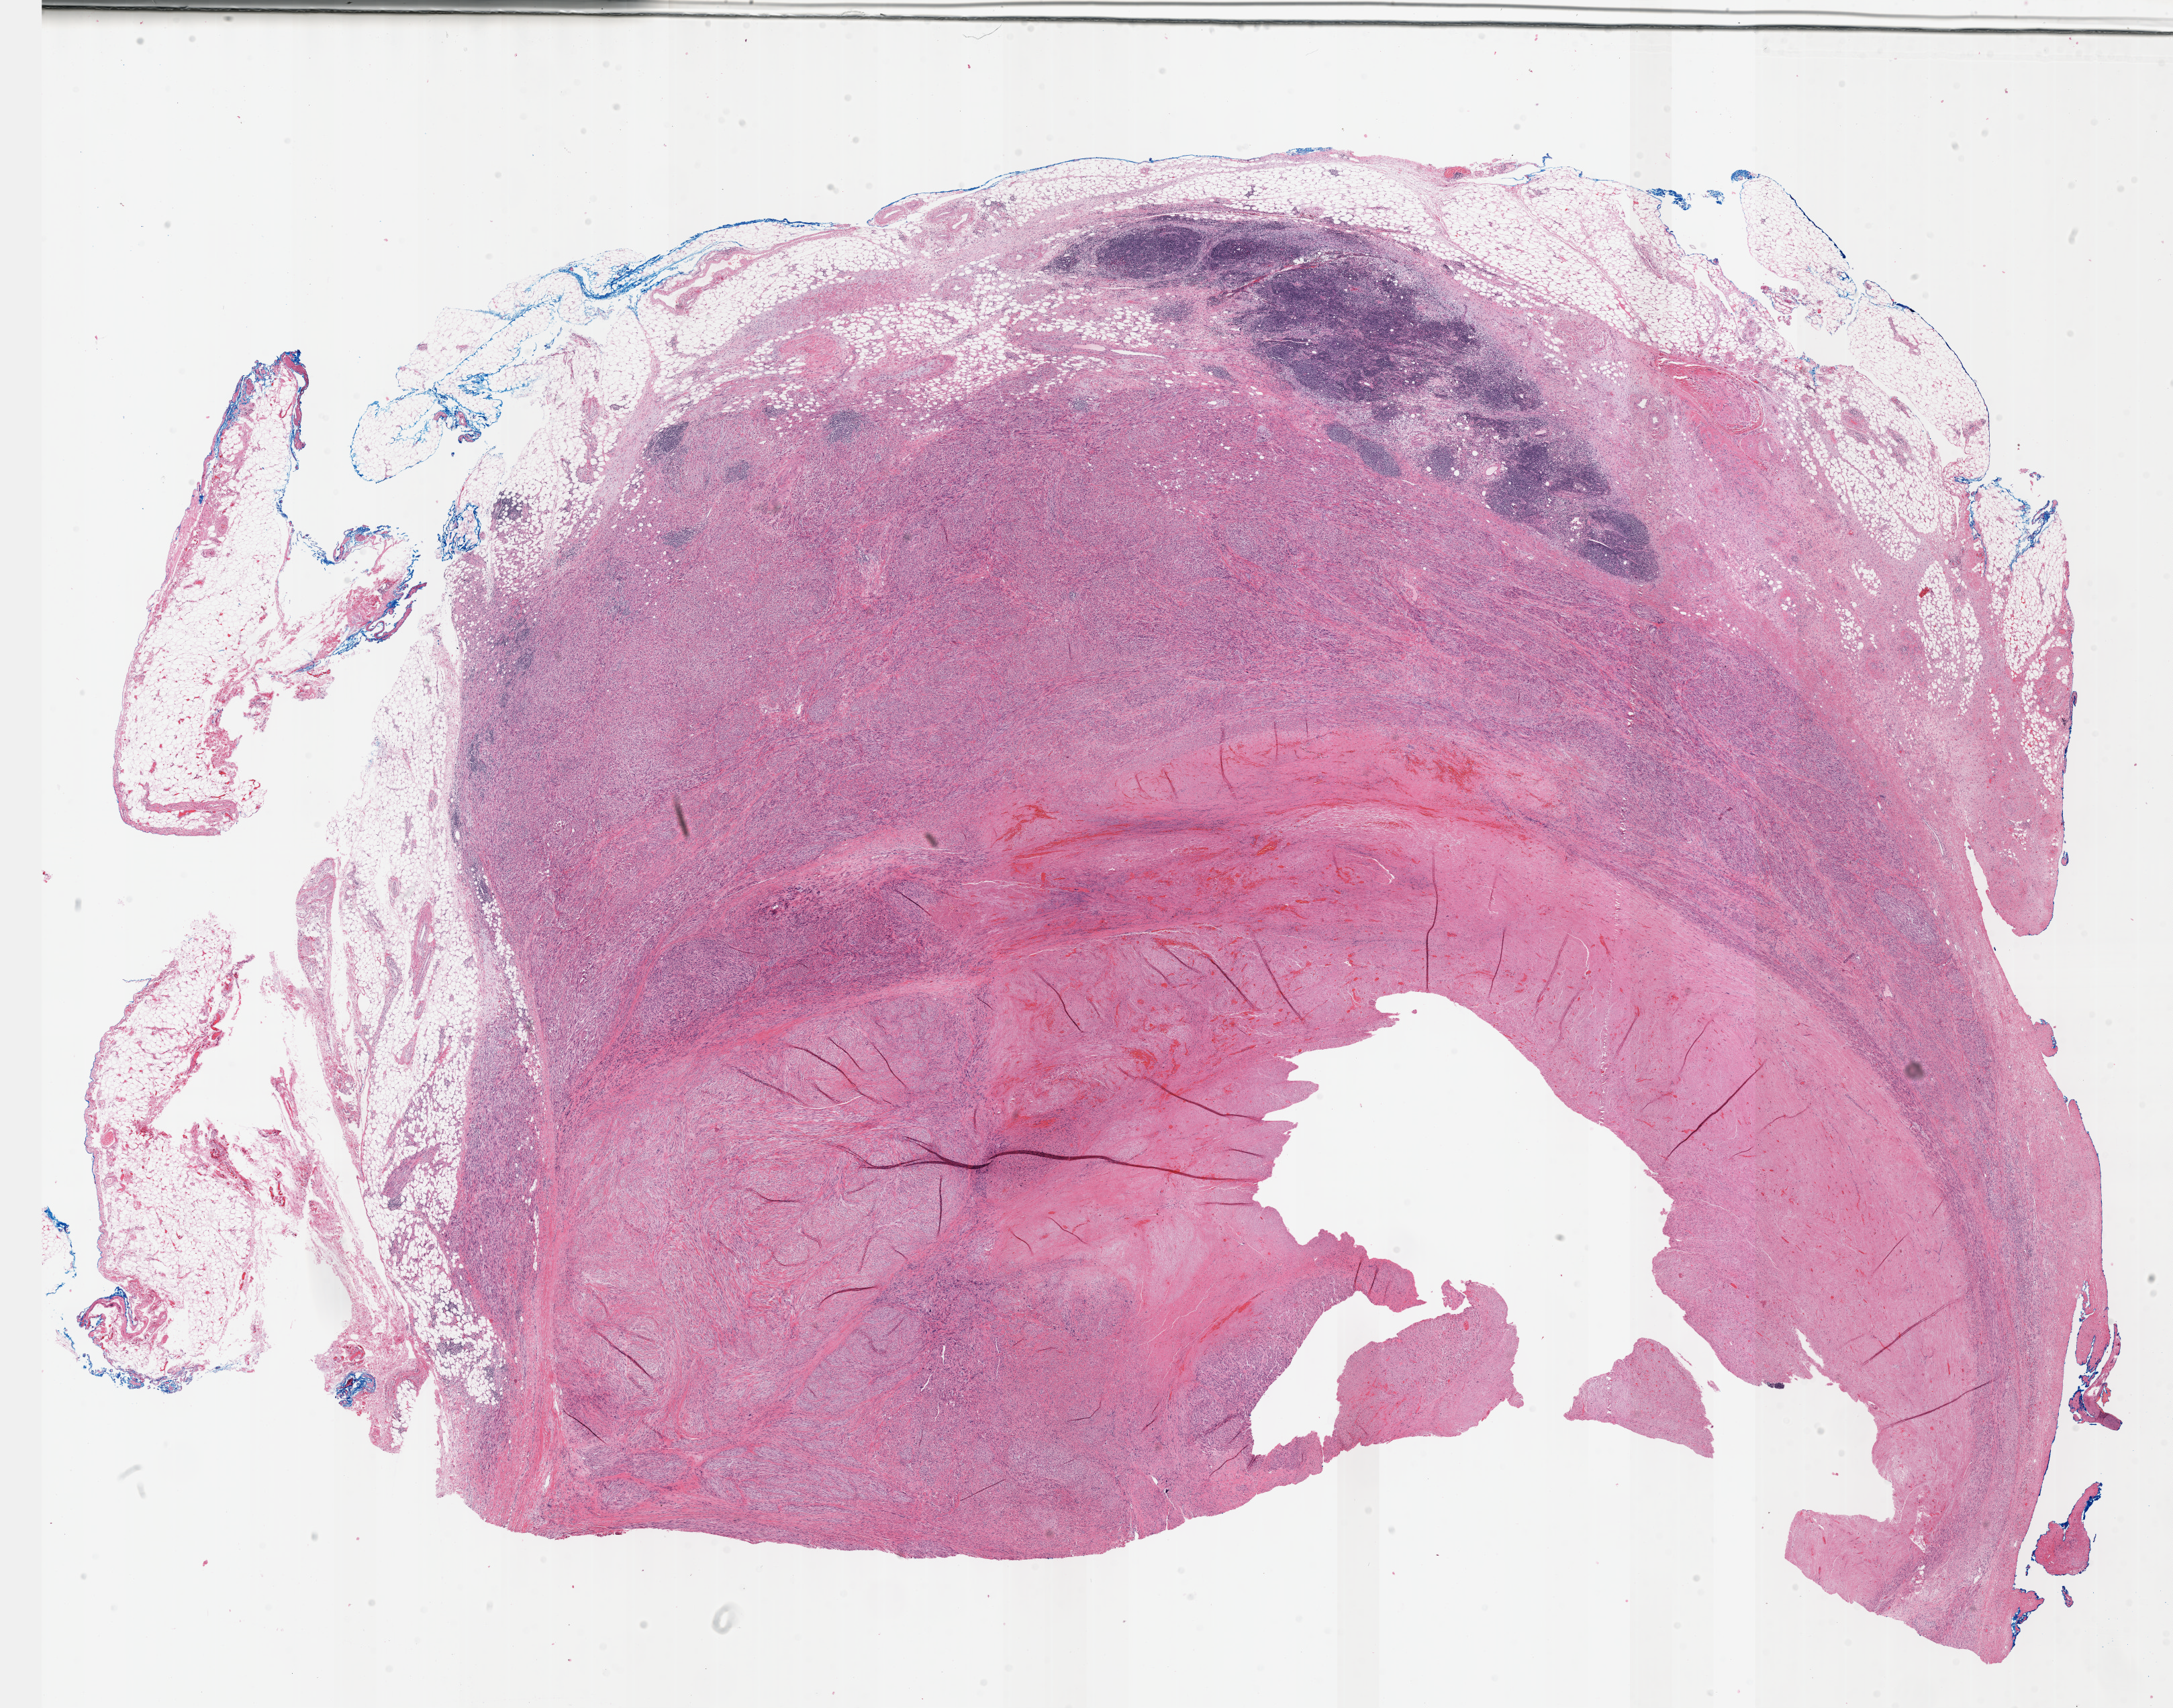
Hematoxylin and eosin (H&E) stained whole-slide image, shown as a low-resolution overview of the whole scanned area (about 26.2 x 20.6 mm, from a 40x scan); FFPE section; connective, subcutaneous and other soft tissues, primary tumour sample. Patient sex: female.
• histologic diagnosis: Leiomyosarcoma, NOS (connective, subcutaneous and other soft tissues of thorax)